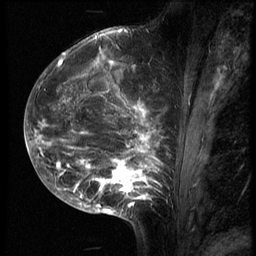
Breast MRI (dynamic contrast-enhanced), one sagittal slice. Slice 27 of 70 in the series (ordered by position). 3 images stored at this slice position (order not interpretable as contrast timing). 1.5 T. TE 4.2 ms, TR 9 ms. 256 × 256 image matrix, field of view 180 × 180 mm. Patient: female, 28 years. From the clinical record (not read from this slice): setting: breast cancer imaged before/during neoadjuvant chemotherapy.
Structures marked on this image (semi-automatically segmented with operator editing):
- analysis volume of interest (the breast-tissue region the enhancement analysis was run in; not a lesion): box from (x=43, y=42) to (x=186, y=215) px
- tumour enhancement mask (voxels above the 140 % enhancement threshold inside the analysis volume of interest): (x=43, y=48)–(x=163, y=214)